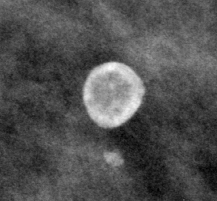
Crop from a digitized film mammogram around one marked abnormality, left breast, MLO view.
Calcifications, morphology round and regular / eggshell; BI-RADS assessment category 2; subtlety rating 3 on a 1 (subtle) to 5 (obvious) scale; benign; no additional work-up was recommended (benign without callback).